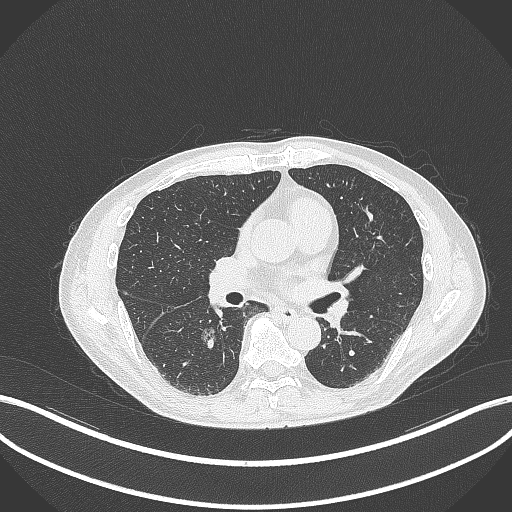
Chest CT, one axial slice; position 168 of 323 along the scan axis; reconstruction kernel B70f; 120 kVp; lung window (W 1500 / L -600 HU); 512 × 512 image matrix, field of view 400 × 400 mm. Patient: male, 61 years. Case-level facts recorded for this patient, not image findings: clinical TNM (as recorded): T1c N0 M0.
Structures marked on this image (rectangle marked by the reading radiologist):
- lung tumour (recorded histology: adenocarcinoma): box from (x=200, y=325) to (x=218, y=343) px